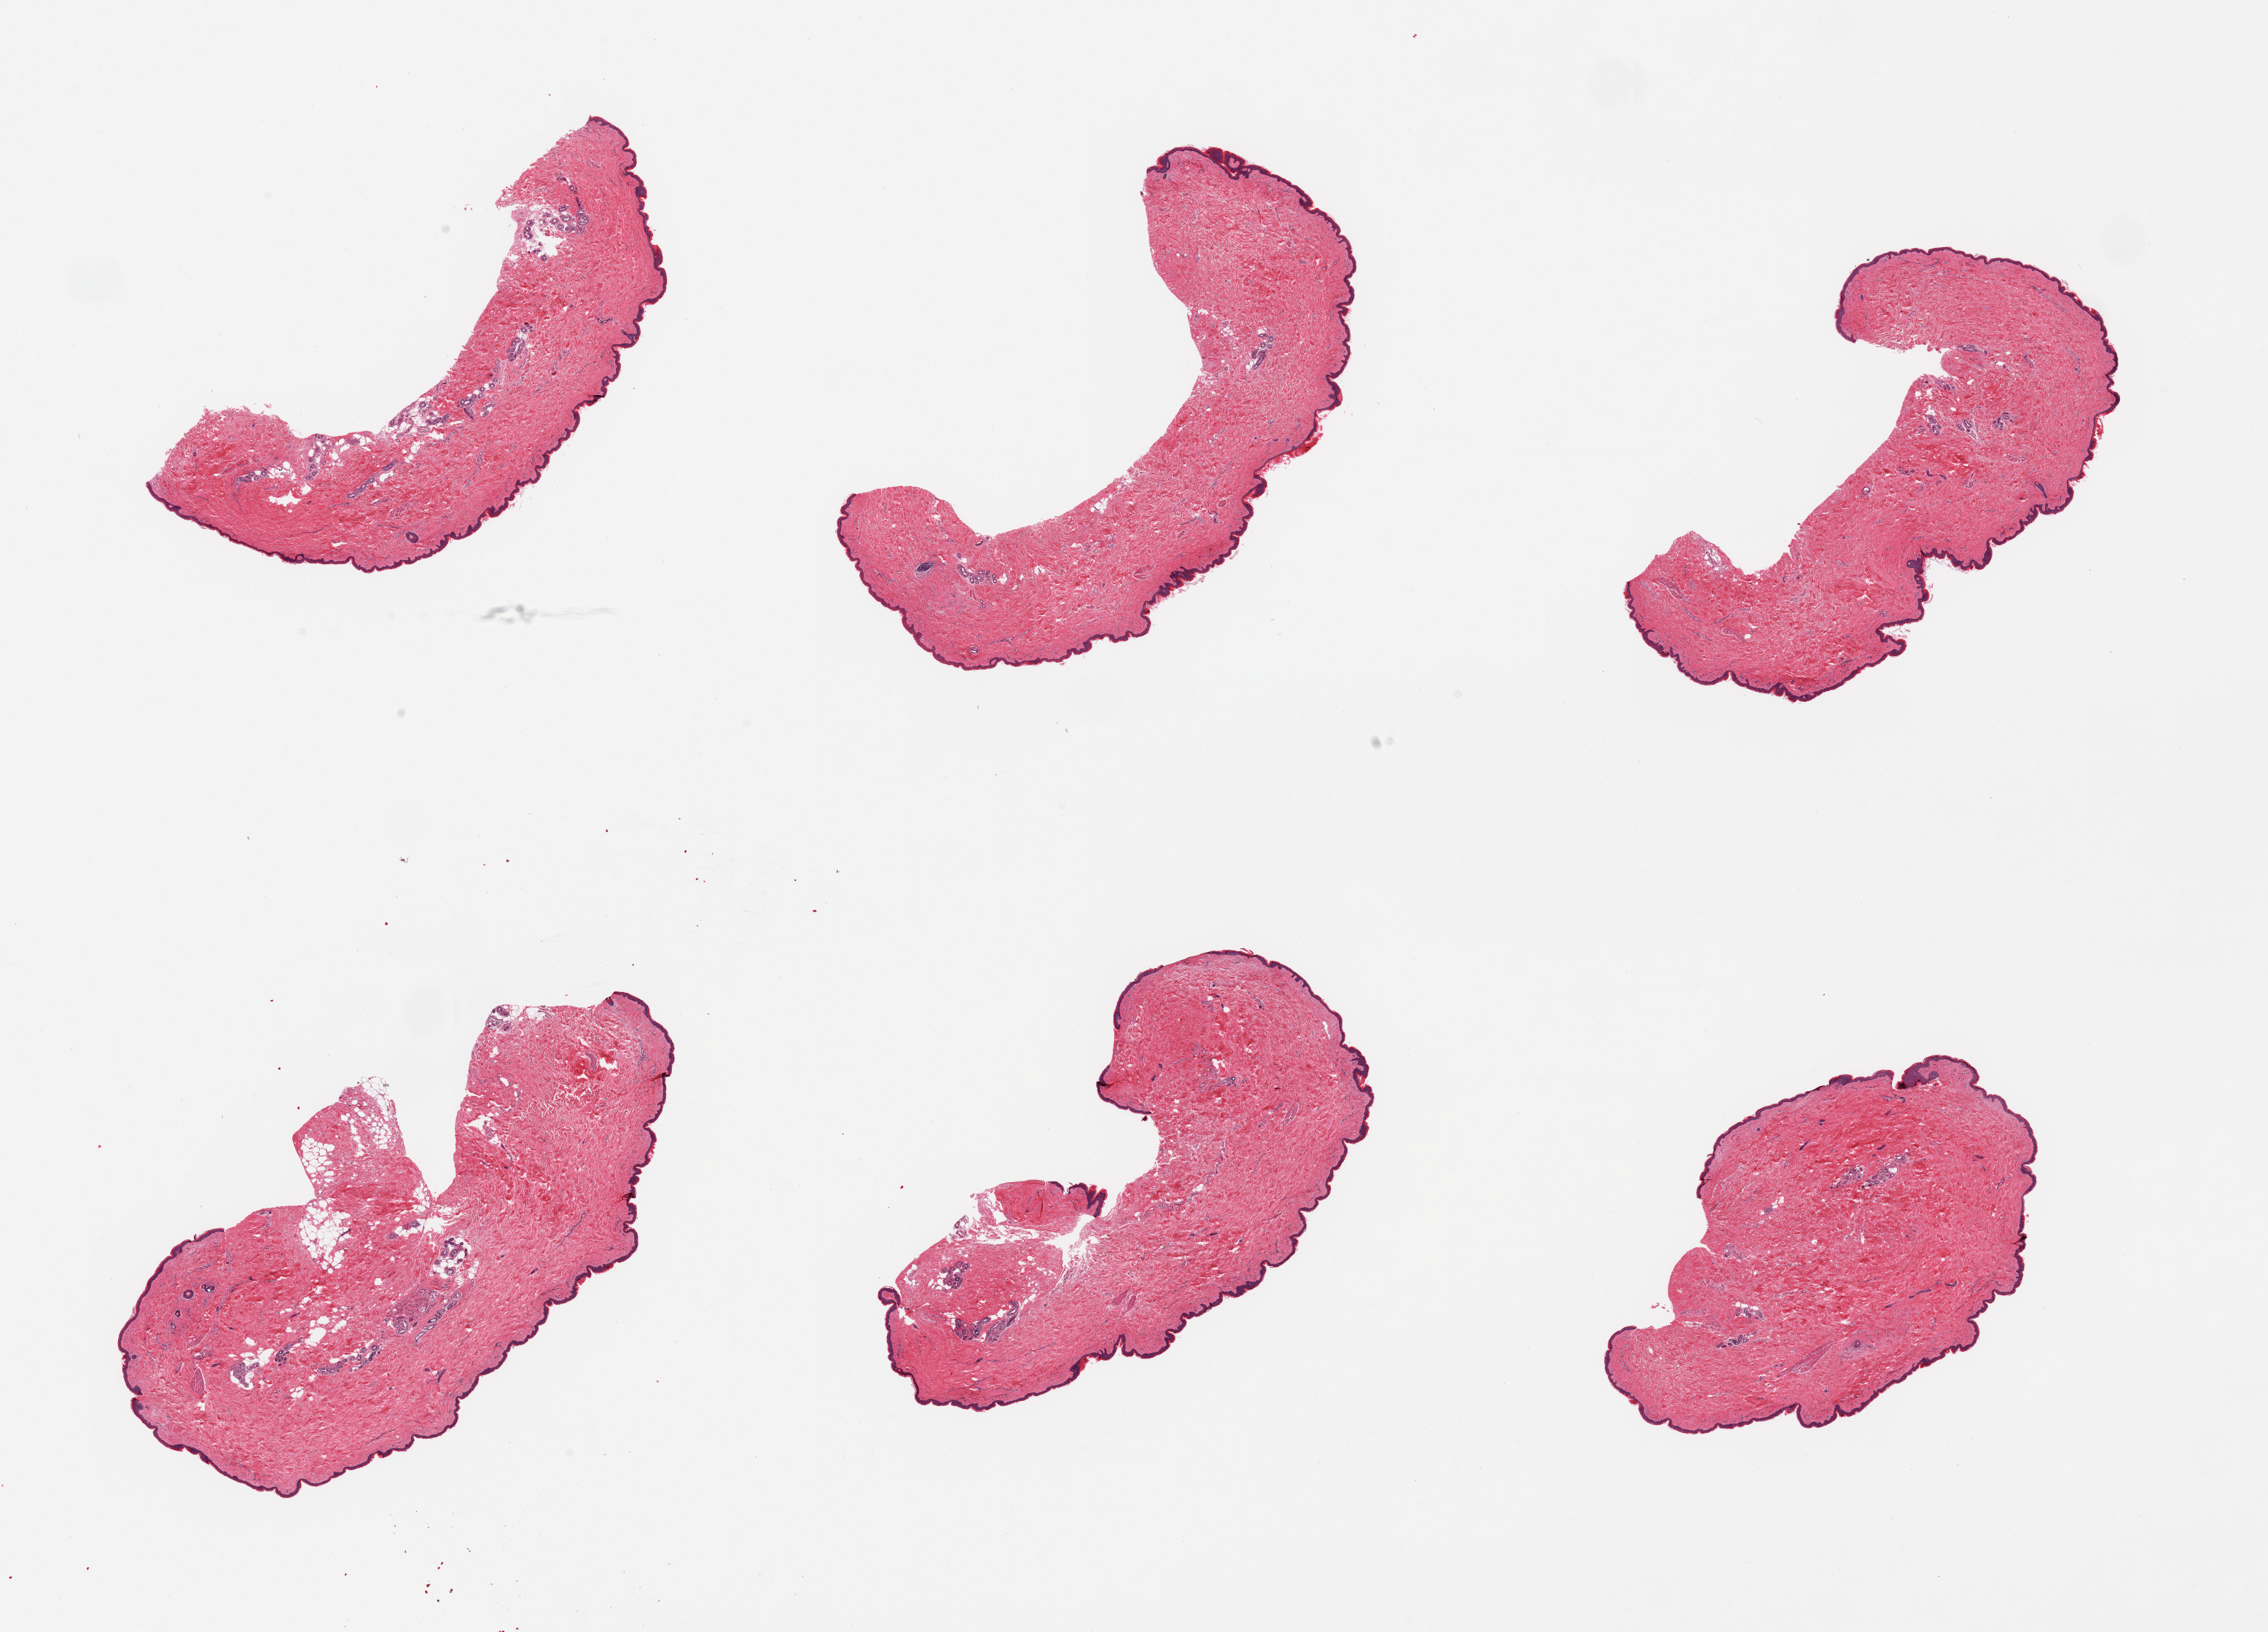
Whole-slide image, haematoxylin and eosin stain, shown as a low-resolution overview of the whole scanned area (about 24.6 x 17.7 mm); PAXgene-fixed, paraffin-embedded tissue; target tissue: skin of suprapubic region; tissue donor sample. Female donor.
• pathologist's review note for this sample: 6 pieces; well trimmed with minimal internal fat